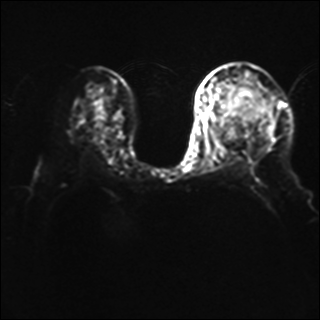
Breast MRI, one axial slice. Position 23 of 40 along the scan axis. Diffusion-weighted series; image 2 of 4 stored at this slice position (different b-values; order by instance number). 1.5 T. 320 × 320 image matrix, field of view 320 × 320 mm. Female patient.
Annotated regions visible in this slice (manually delineated by an expert):
- tumour on diffusion-weighted imaging: box from (x=238, y=86) to (x=257, y=110) px